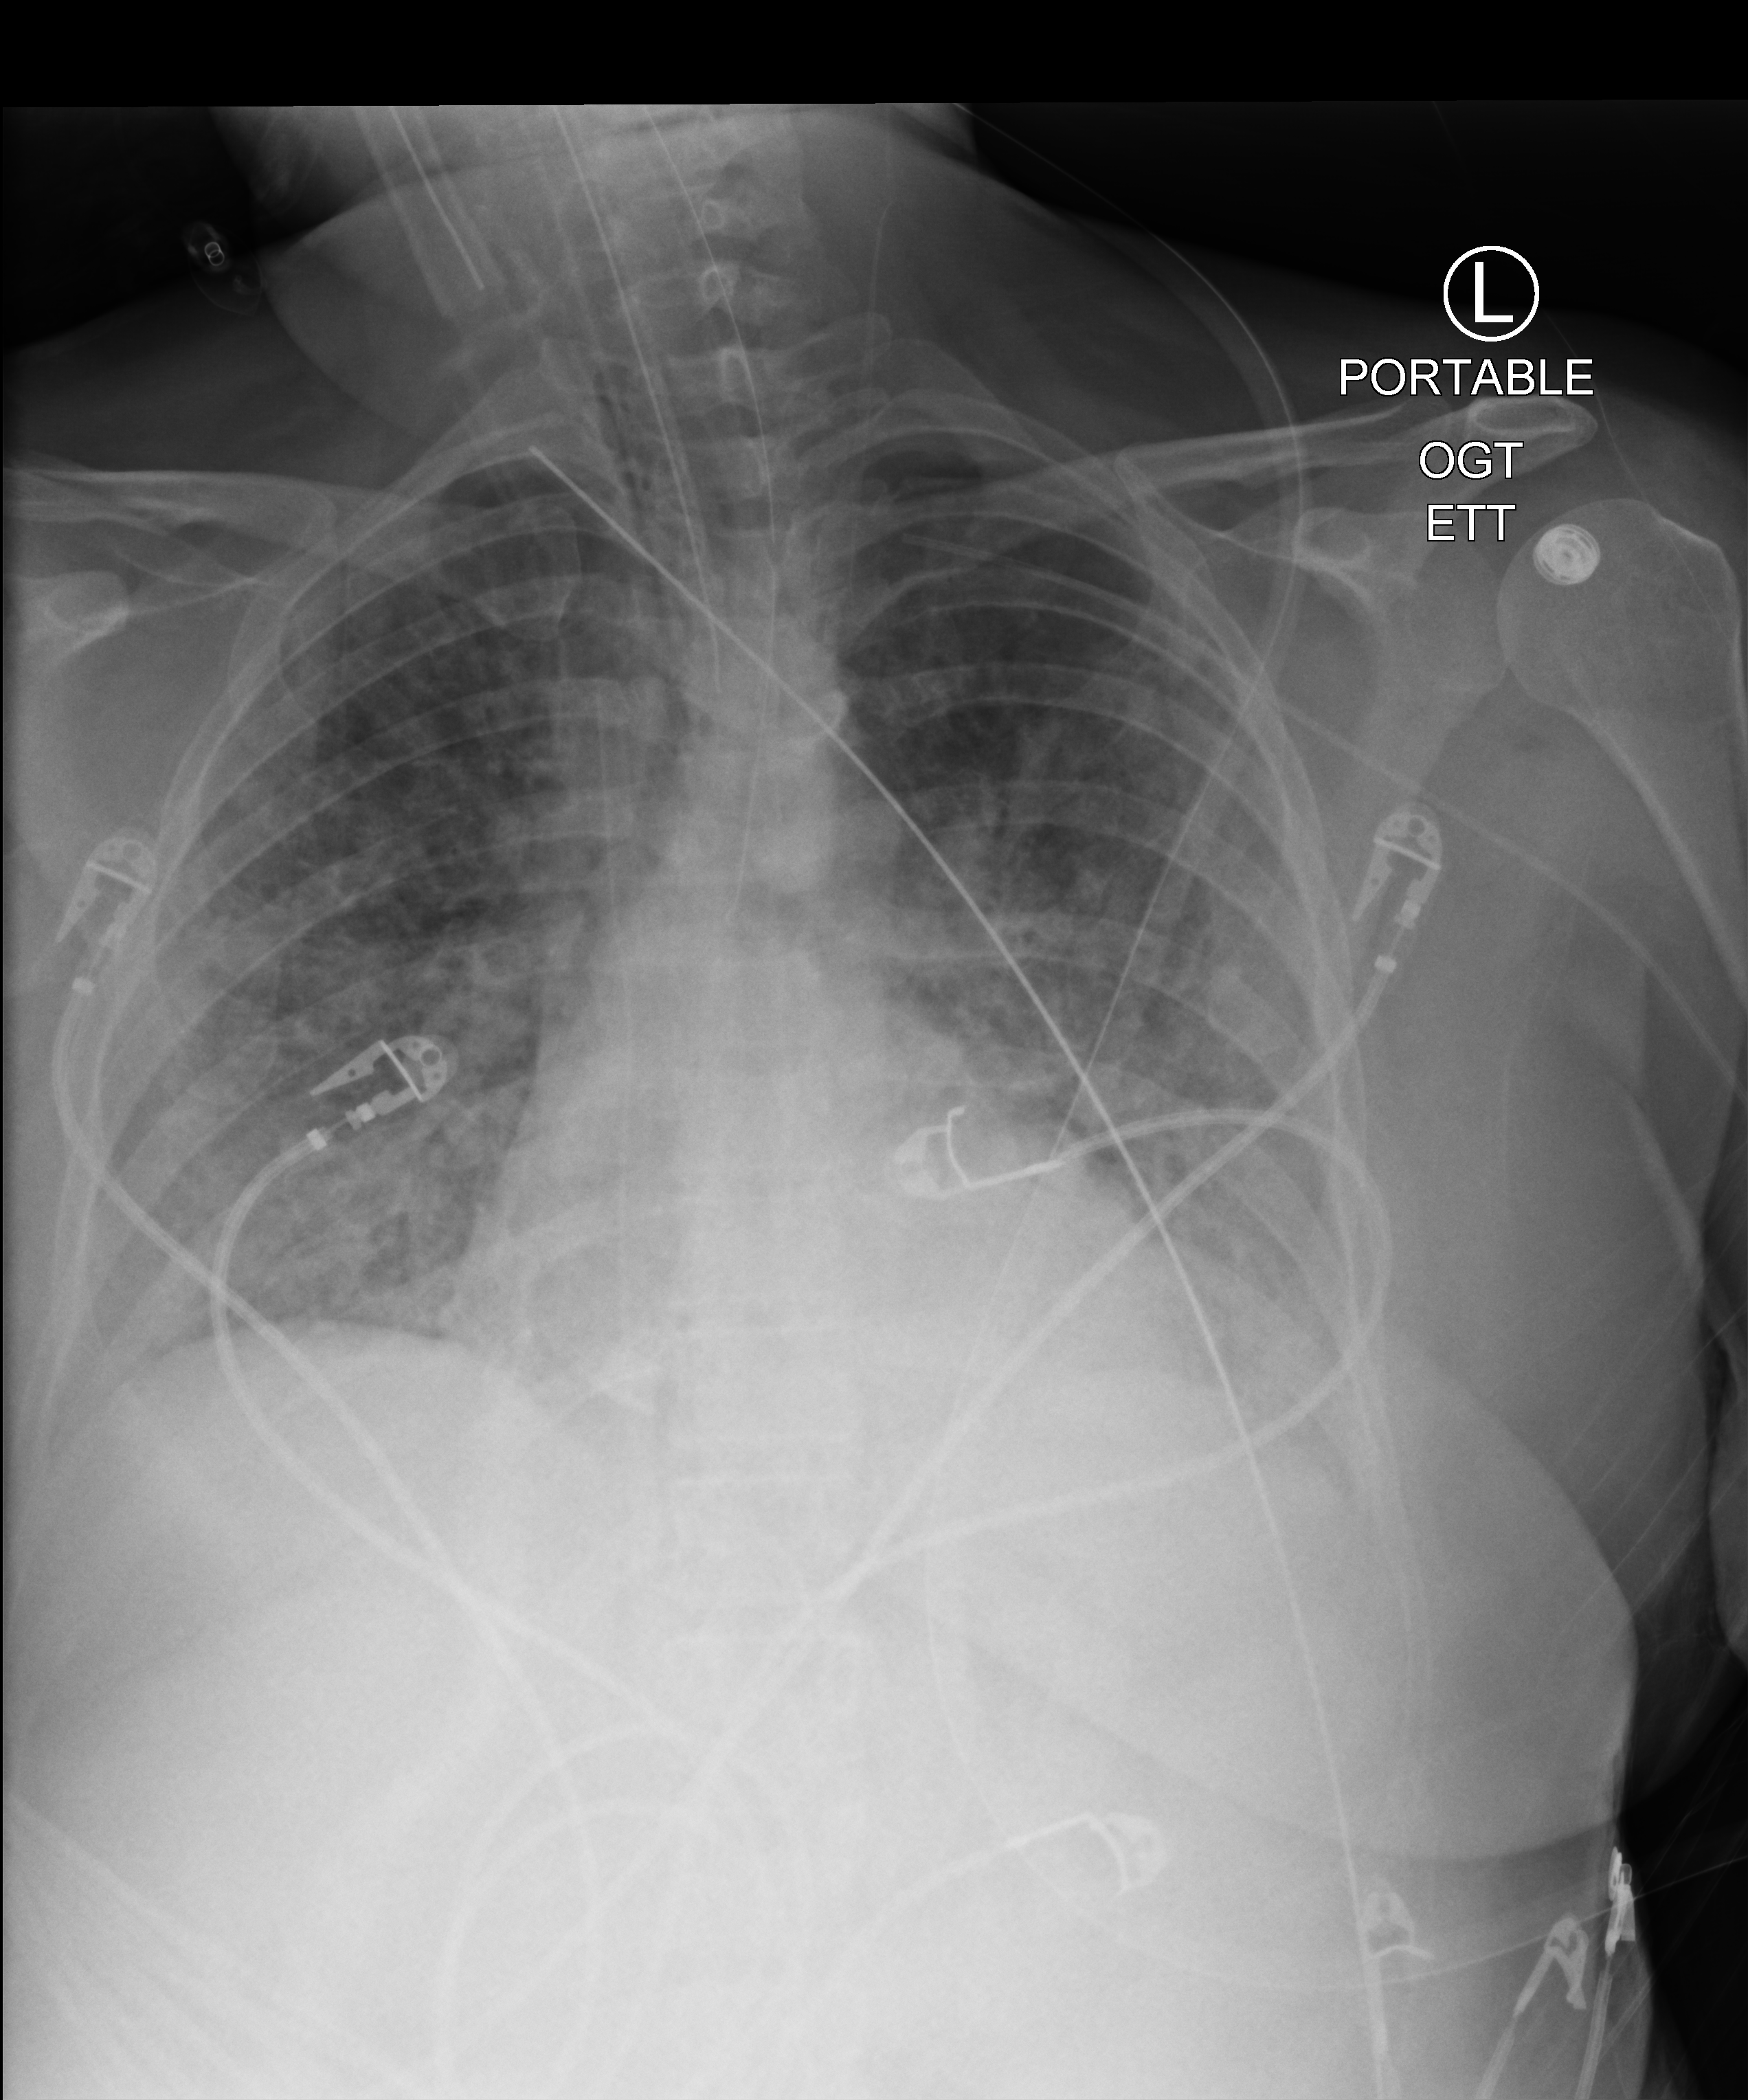
Chest X-ray (portable); anteroposterior (AP) projection. Female patient hospitalised with COVID-19, age 18–59 years.
From the hospital-stay record, not from the radiograph (when in the stay this image was taken is not recorded): length of hospital stay: 31 days; hypertension (admission record): yes; mechanically ventilated during this hospital stay: yes.